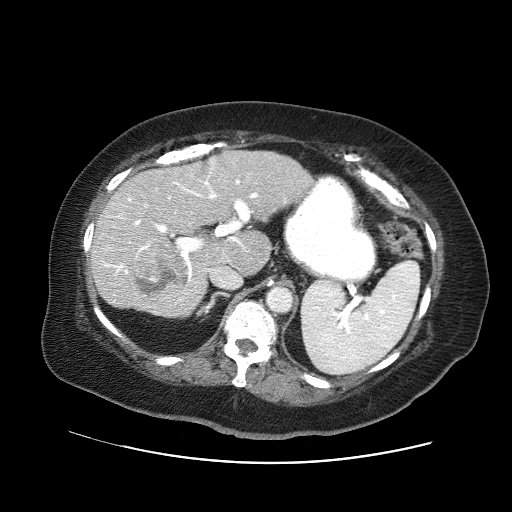
Contrast-enhanced abdominal CT (liver protocol), one axial slice; position 33 of 71 along the scan axis; reconstruction kernel STANDARD; 120 kVp; soft-tissue window (W 400 / L 40 HU); 512 × 512 image matrix, field of view 400 × 400 mm. Case-level facts recorded for this patient, not image findings: diagnosis: hepatocellular carcinoma (patient treated with transarterial chemoembolisation; whether this scan precedes or follows treatment is not stated here); TNM stage (as recorded): Stage-II; Child-Pugh class: A; tumour nodularity: multinodular.
Outlined on this slice (semi-automatically segmented with operator editing):
- liver parenchyma outside the tumour (the mass and vessels are separate outlines, so this box may not span the whole liver): bounding box [x1, y1, x2, y2] px = [90, 150, 312, 316]
- mass: [134, 243, 190, 297]
- liver vessels: [103, 161, 258, 300]